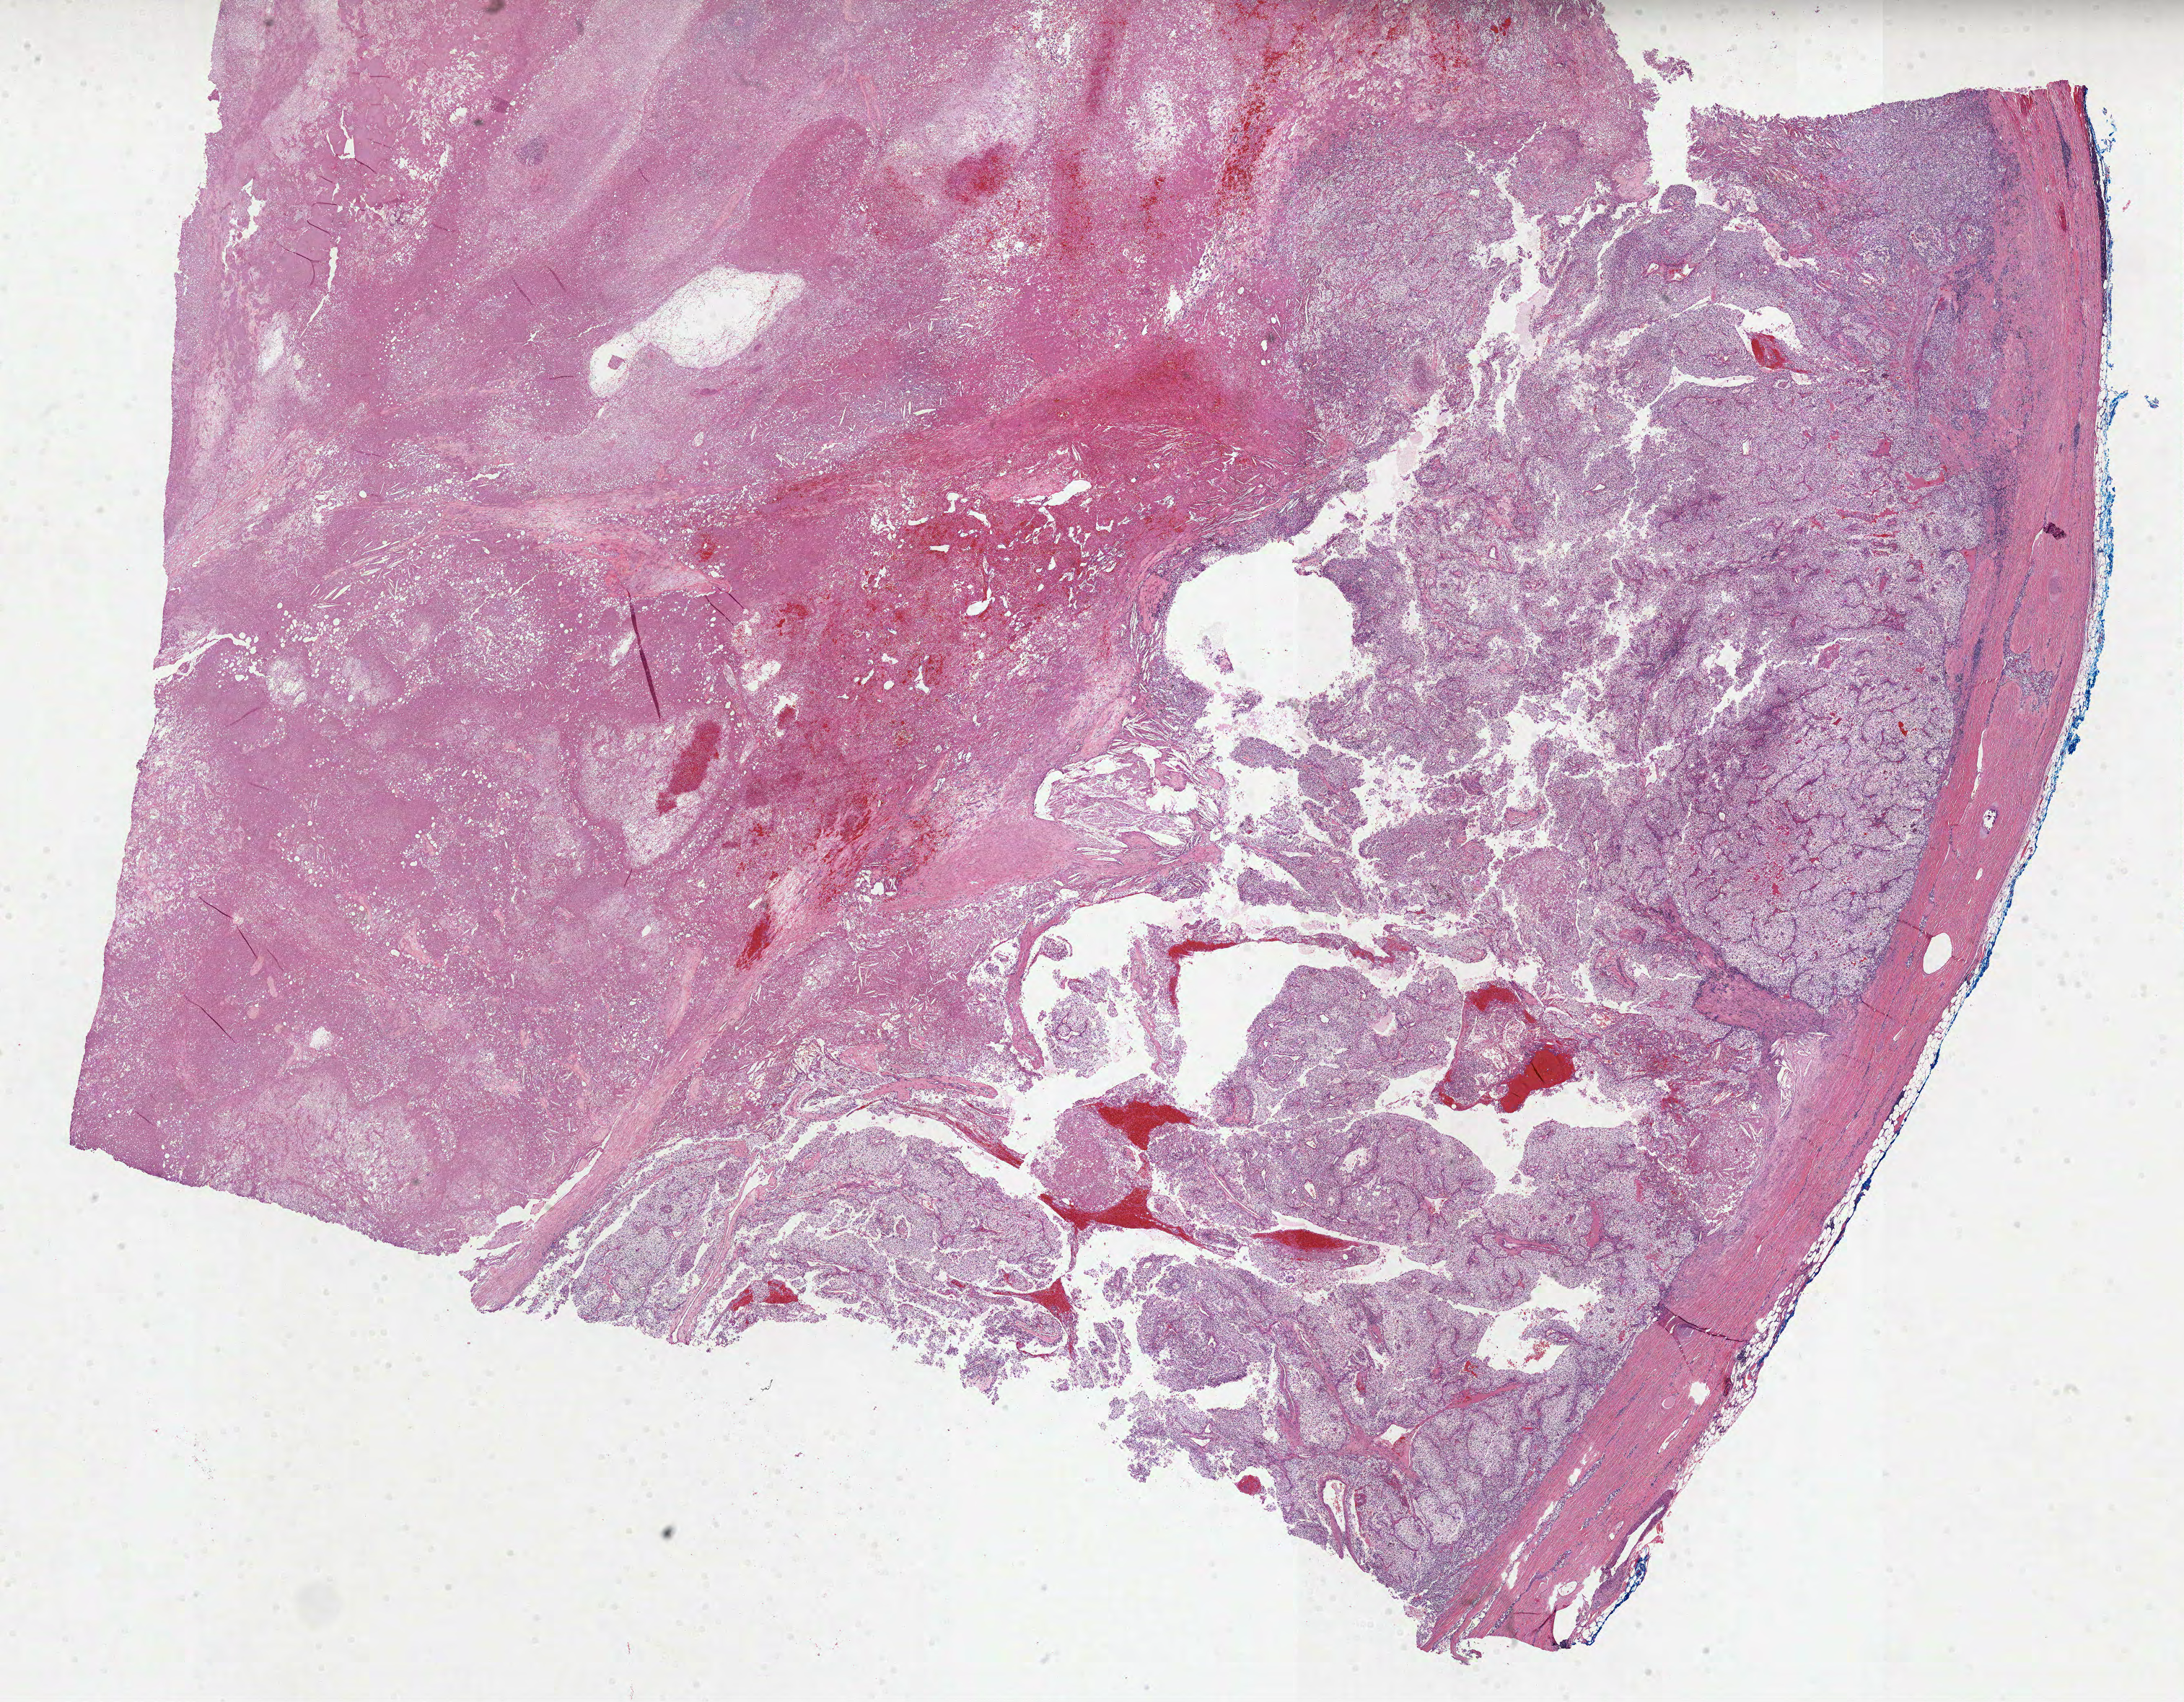
Digitized H&E tissue section (whole slide), shown as a low-resolution overview of the whole scanned area (about 24.4 x 19.0 mm); FFPE section; primary tumour sample from the kidney. Male patient; age at initial diagnosis 62 years. Histologic grade: G2 (moderately differentiated).
AJCC pathologic stage: IV. Diagnosis: Clear cell adenocarcinoma, NOS.